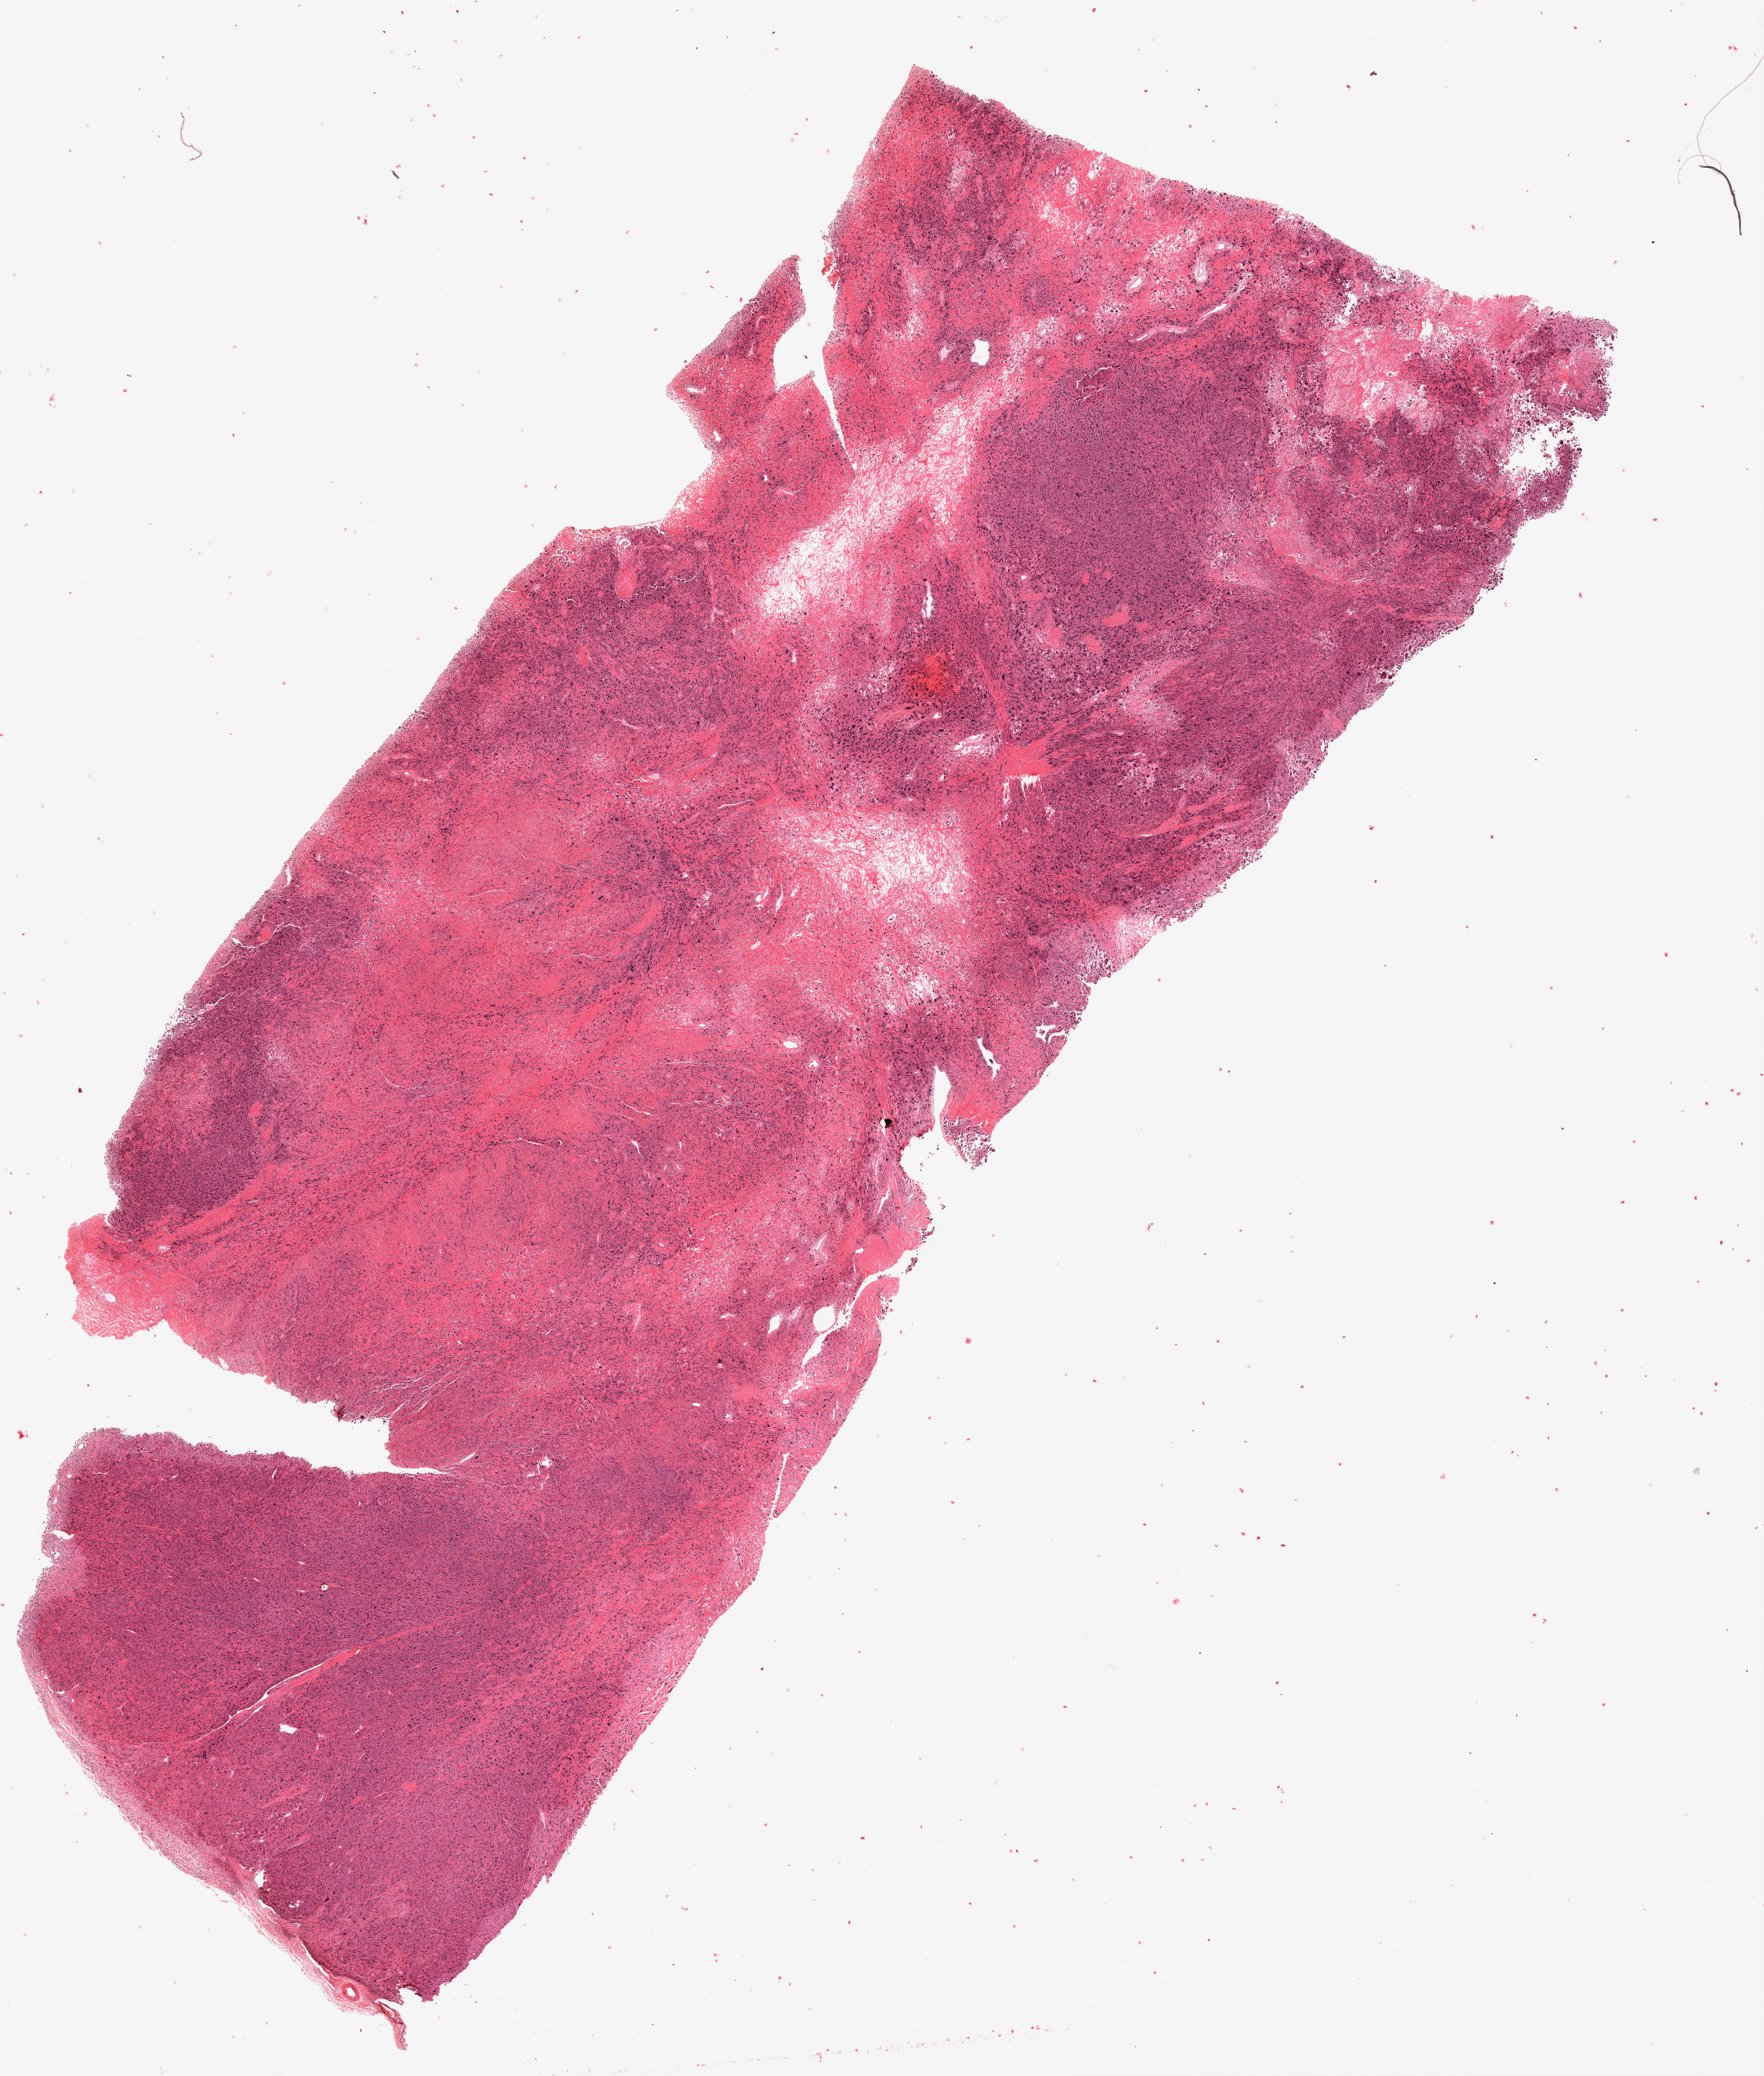
Digitized H&E tissue section (whole slide) — a low-resolution overview of the entire scanned area, about 18.0 x 21.1 mm. Formalin-fixed paraffin-embedded (FFPE) diagnostic section. Sample: primary tumour, connective, subcutaneous and other soft tissues. Female patient; age at initial diagnosis 60 years.
Histologic diagnosis: Undifferentiated sarcoma (connective, subcutaneous and other soft tissues of lower limb and hip).